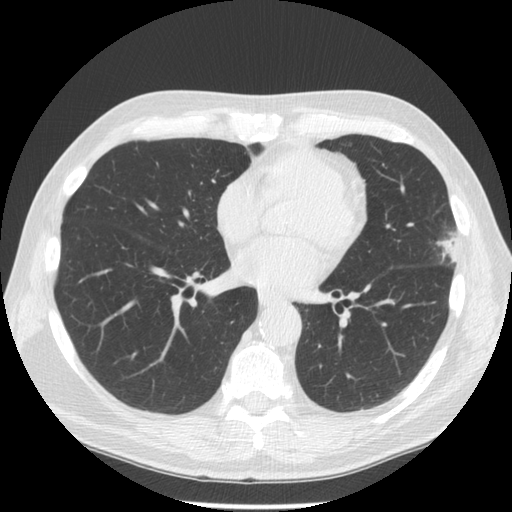
Low-dose screening chest CT, one axial slice. Slice 64 of 134 in the series (ordered by position). Reconstruction kernel STANDARD. 120 kVp. Lung window (W 1500 / L -600 HU). 512 × 512 image matrix, field of view 350 × 350 mm.
Annotated regions visible in this slice (expert manual segmentation):
- lesion 1 (tumor, upper lobe of left lung): bounding box <440,235,459,262> (left, top, right, bottom; pixels)